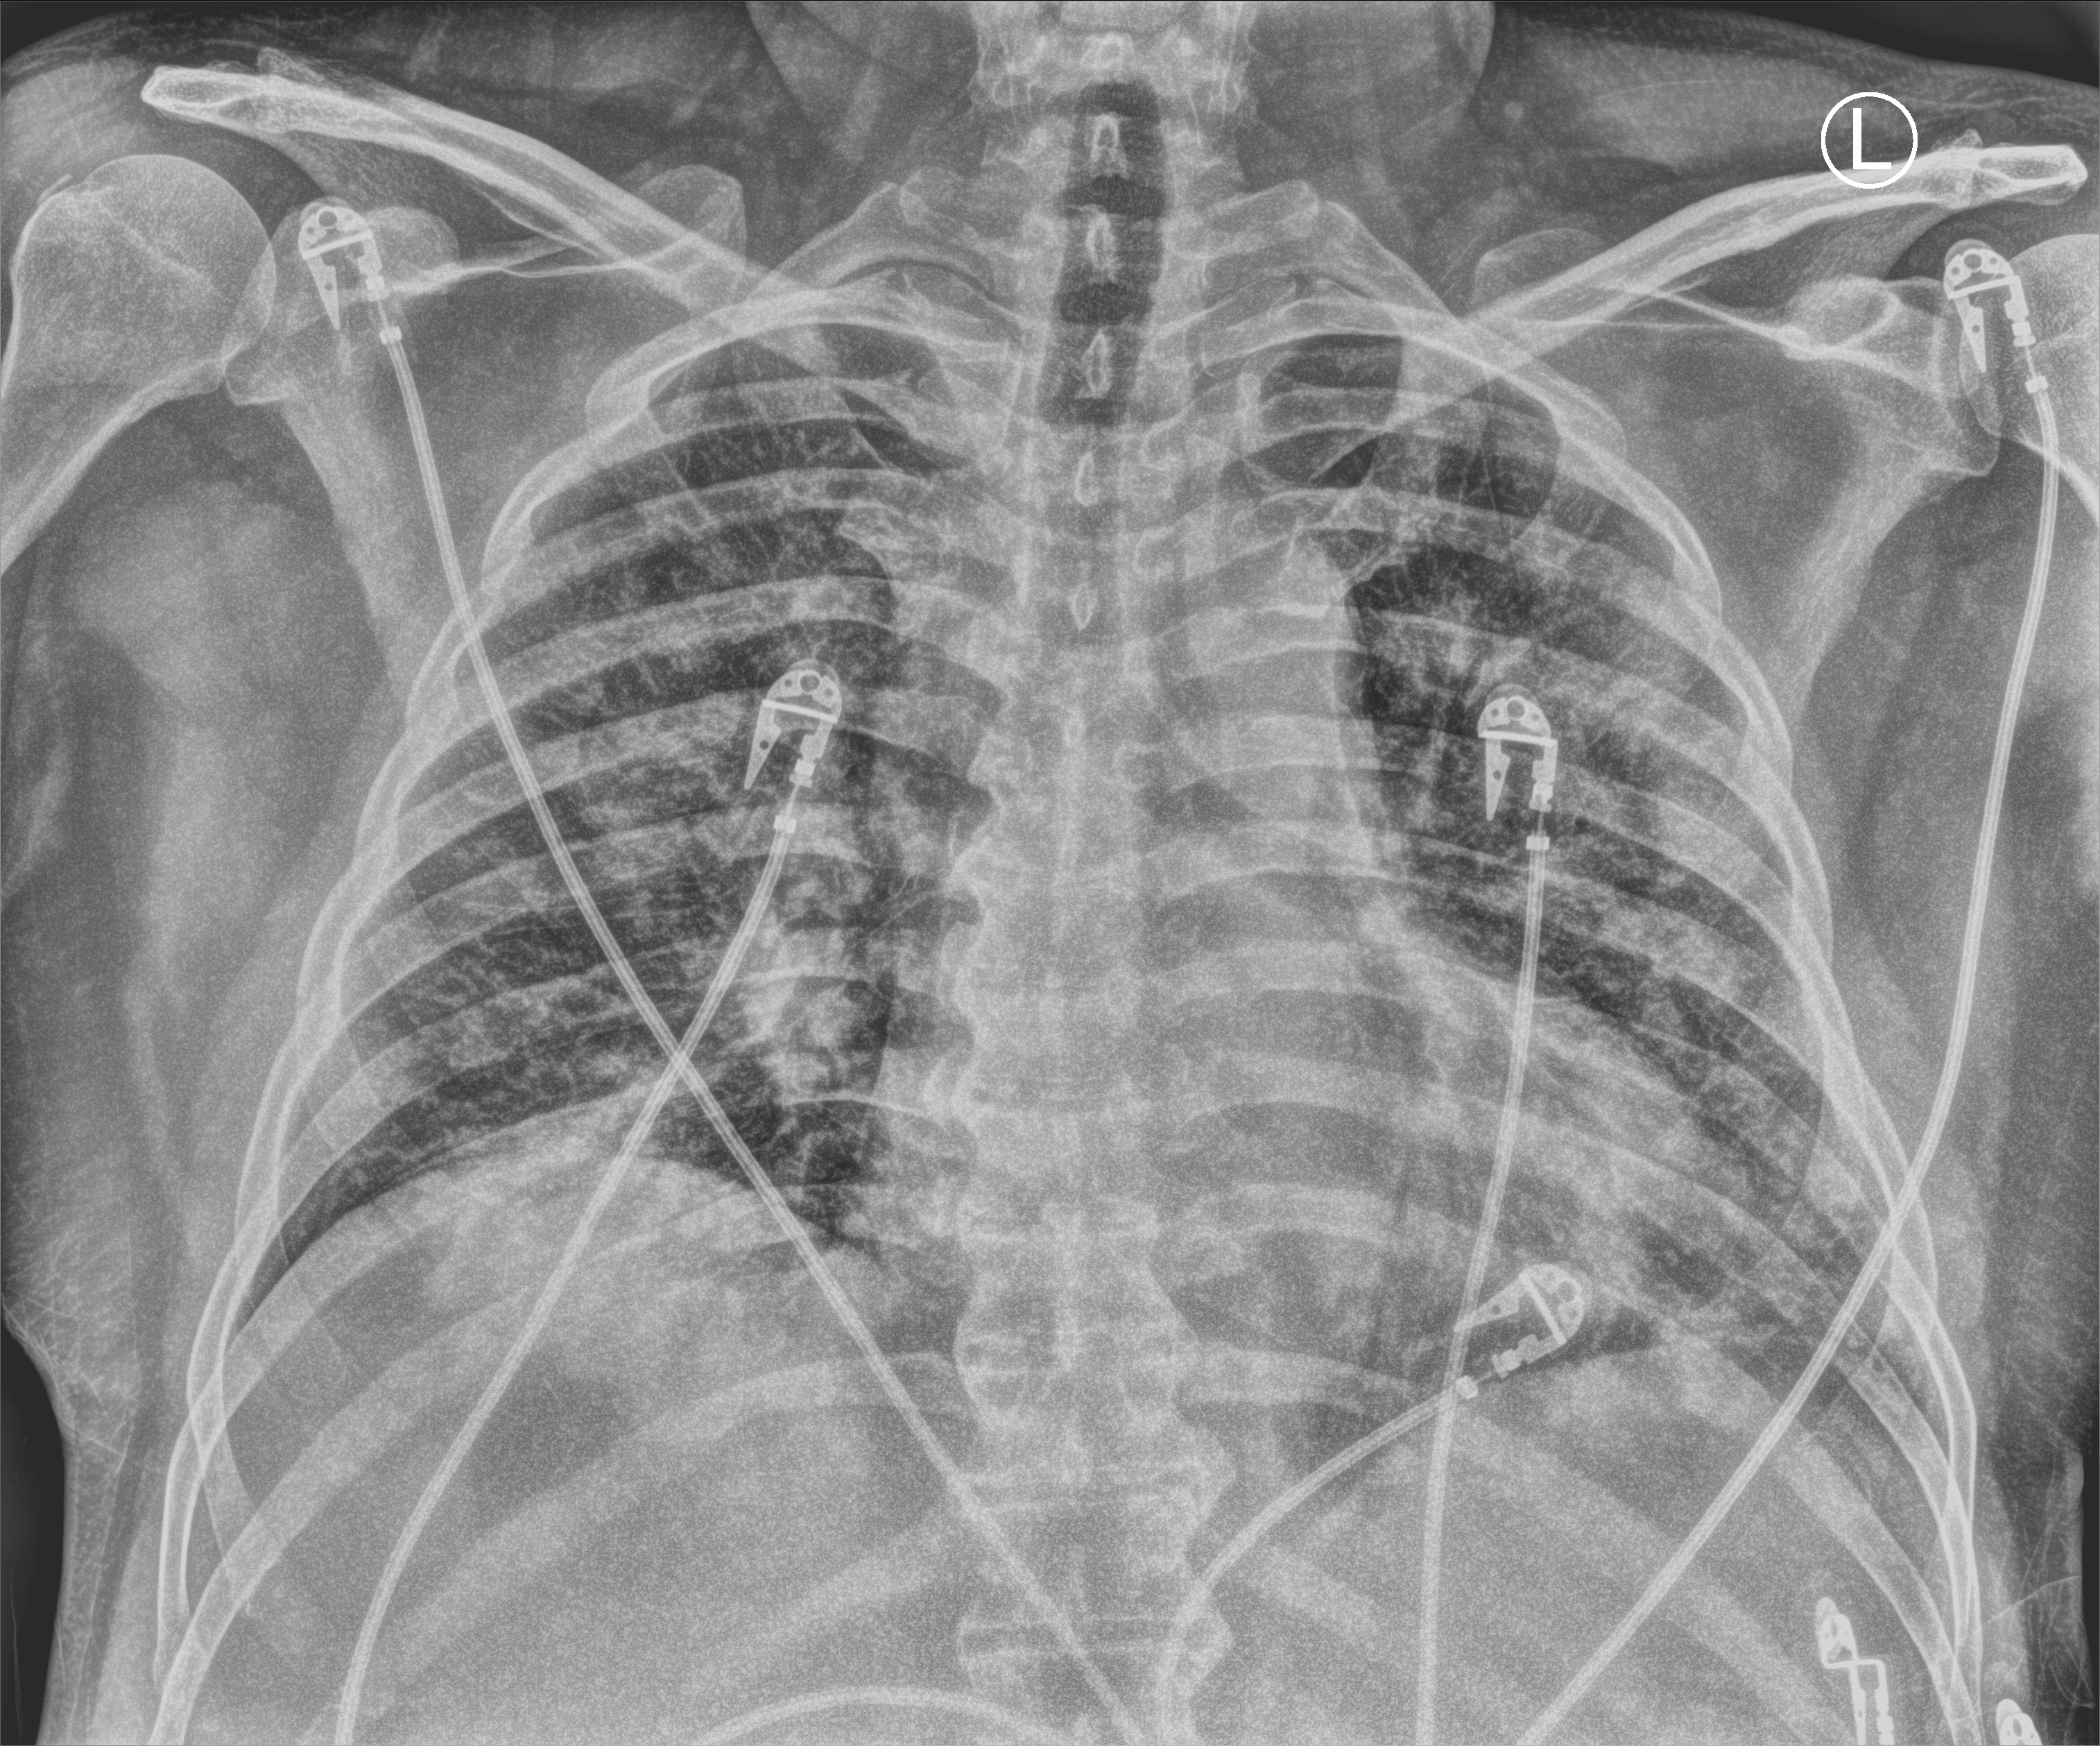
Portable chest radiograph; anteroposterior (AP) projection. Male patient hospitalised with COVID-19, age 18–59 years.
Admission-level facts for this patient (not findings on this image; timing relative to this image not recorded):
- admitted to intensive care during this hospital stay: yes